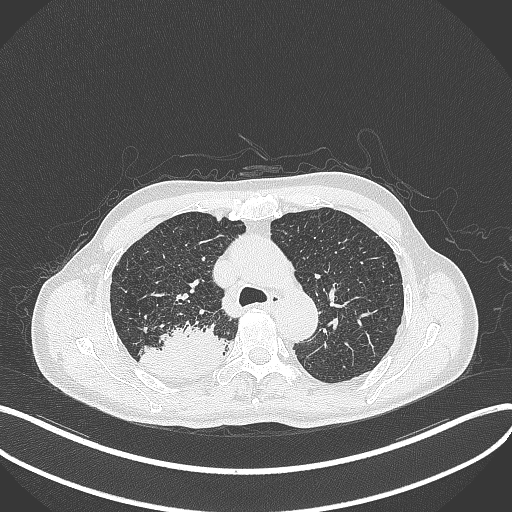
Chest CT, one axial slice. Lung window (W 1500 / L -600 HU). 512 × 512 image matrix. Patient: male, 79 years. From the clinical record (not read from this slice): clinical TNM (as recorded): T3 N0 M0.
Outlined on this slice (bounding box drawn by a radiologist):
- lung tumour (recorded histology: adenocarcinoma): bounding box [x1, y1, x2, y2] px = [137, 319, 228, 374]